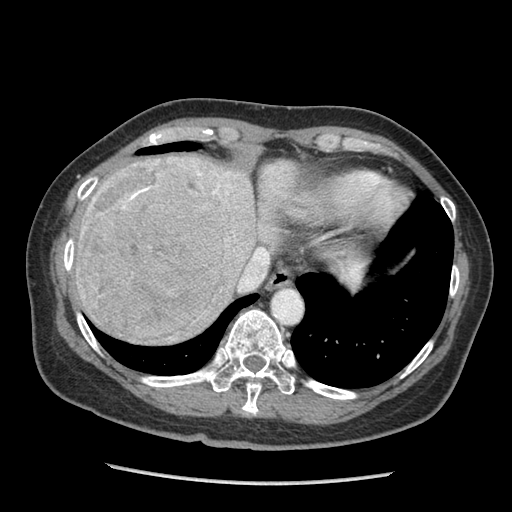
Contrast-enhanced abdominal CT (liver protocol), one axial slice. Position 77 of 105 along the scan axis. Reconstruction kernel STANDARD. 140 kVp. Soft-tissue window (W 400 / L 40 HU). 2.5 mm slice thickness. 512 × 512 image matrix. Case-level facts recorded for this patient, not image findings: diagnosis: hepatocellular carcinoma (patient treated with transarterial chemoembolisation; whether this scan precedes or follows treatment is not stated here); TNM stage (as recorded): Stage-I; Child-Pugh class: A.
Outlined on this slice (semi-automatic segmentation, software-assisted and operator-edited):
- liver parenchyma outside the tumour (the mass and vessels are separate outlines, so this box may not span the whole liver): bounding box (x1, y1, x2, y2) in pixels: (72, 154, 296, 334)
- mass: (76, 157, 232, 344)
- liver vessels: (93, 185, 228, 201)